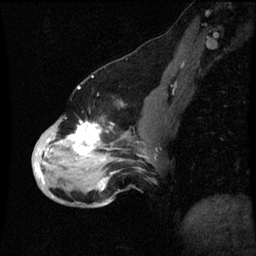
Breast MRI (dynamic contrast-enhanced), one sagittal slice. Slice 25 of 60 in the series (ordered by position). Dynamic contrast-enhanced series, image 2 of 3 at this slice position (ordered by acquisition). 1.5 T. TE 4.2 ms, TR 8.9 ms. 2 mm slice thickness. 256 × 256 image matrix, field of view 200 × 200 mm. Female patient, age 49 years. From the clinical record (not read from this slice): setting: breast cancer imaged before/during neoadjuvant chemotherapy; receptor status: HR-positive, HER2-negative.
Annotated regions visible in this slice (semi-automatically segmented with operator editing):
- analysis volume of interest (the breast-tissue region the enhancement analysis was run in; not a lesion): bounding box <32,102,153,199> (left, top, right, bottom; pixels)
- tumour enhancement mask (voxels above the 70 % enhancement threshold inside the analysis volume of interest): <36,122,103,179>